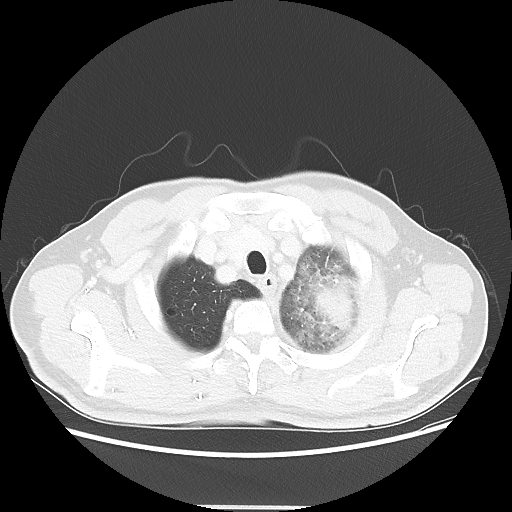
Chest CT, one axial slice. Slice 50 of 53 in the series (ordered by position). 100 kVp. Lung window (W 1500 / L -600 HU). 5 mm slice thickness. 512 × 512 image matrix, field of view 391 × 391 mm. Patient: male, 60 years. From the clinical record (not read from this slice): clinical TNM (as recorded): T4 N1 M1a; histopathological grade: G3.
Outlined on this slice (bounding box drawn by a radiologist):
- lung tumour (recorded histology: large cell carcinoma): box from (x=311, y=270) to (x=373, y=334) px